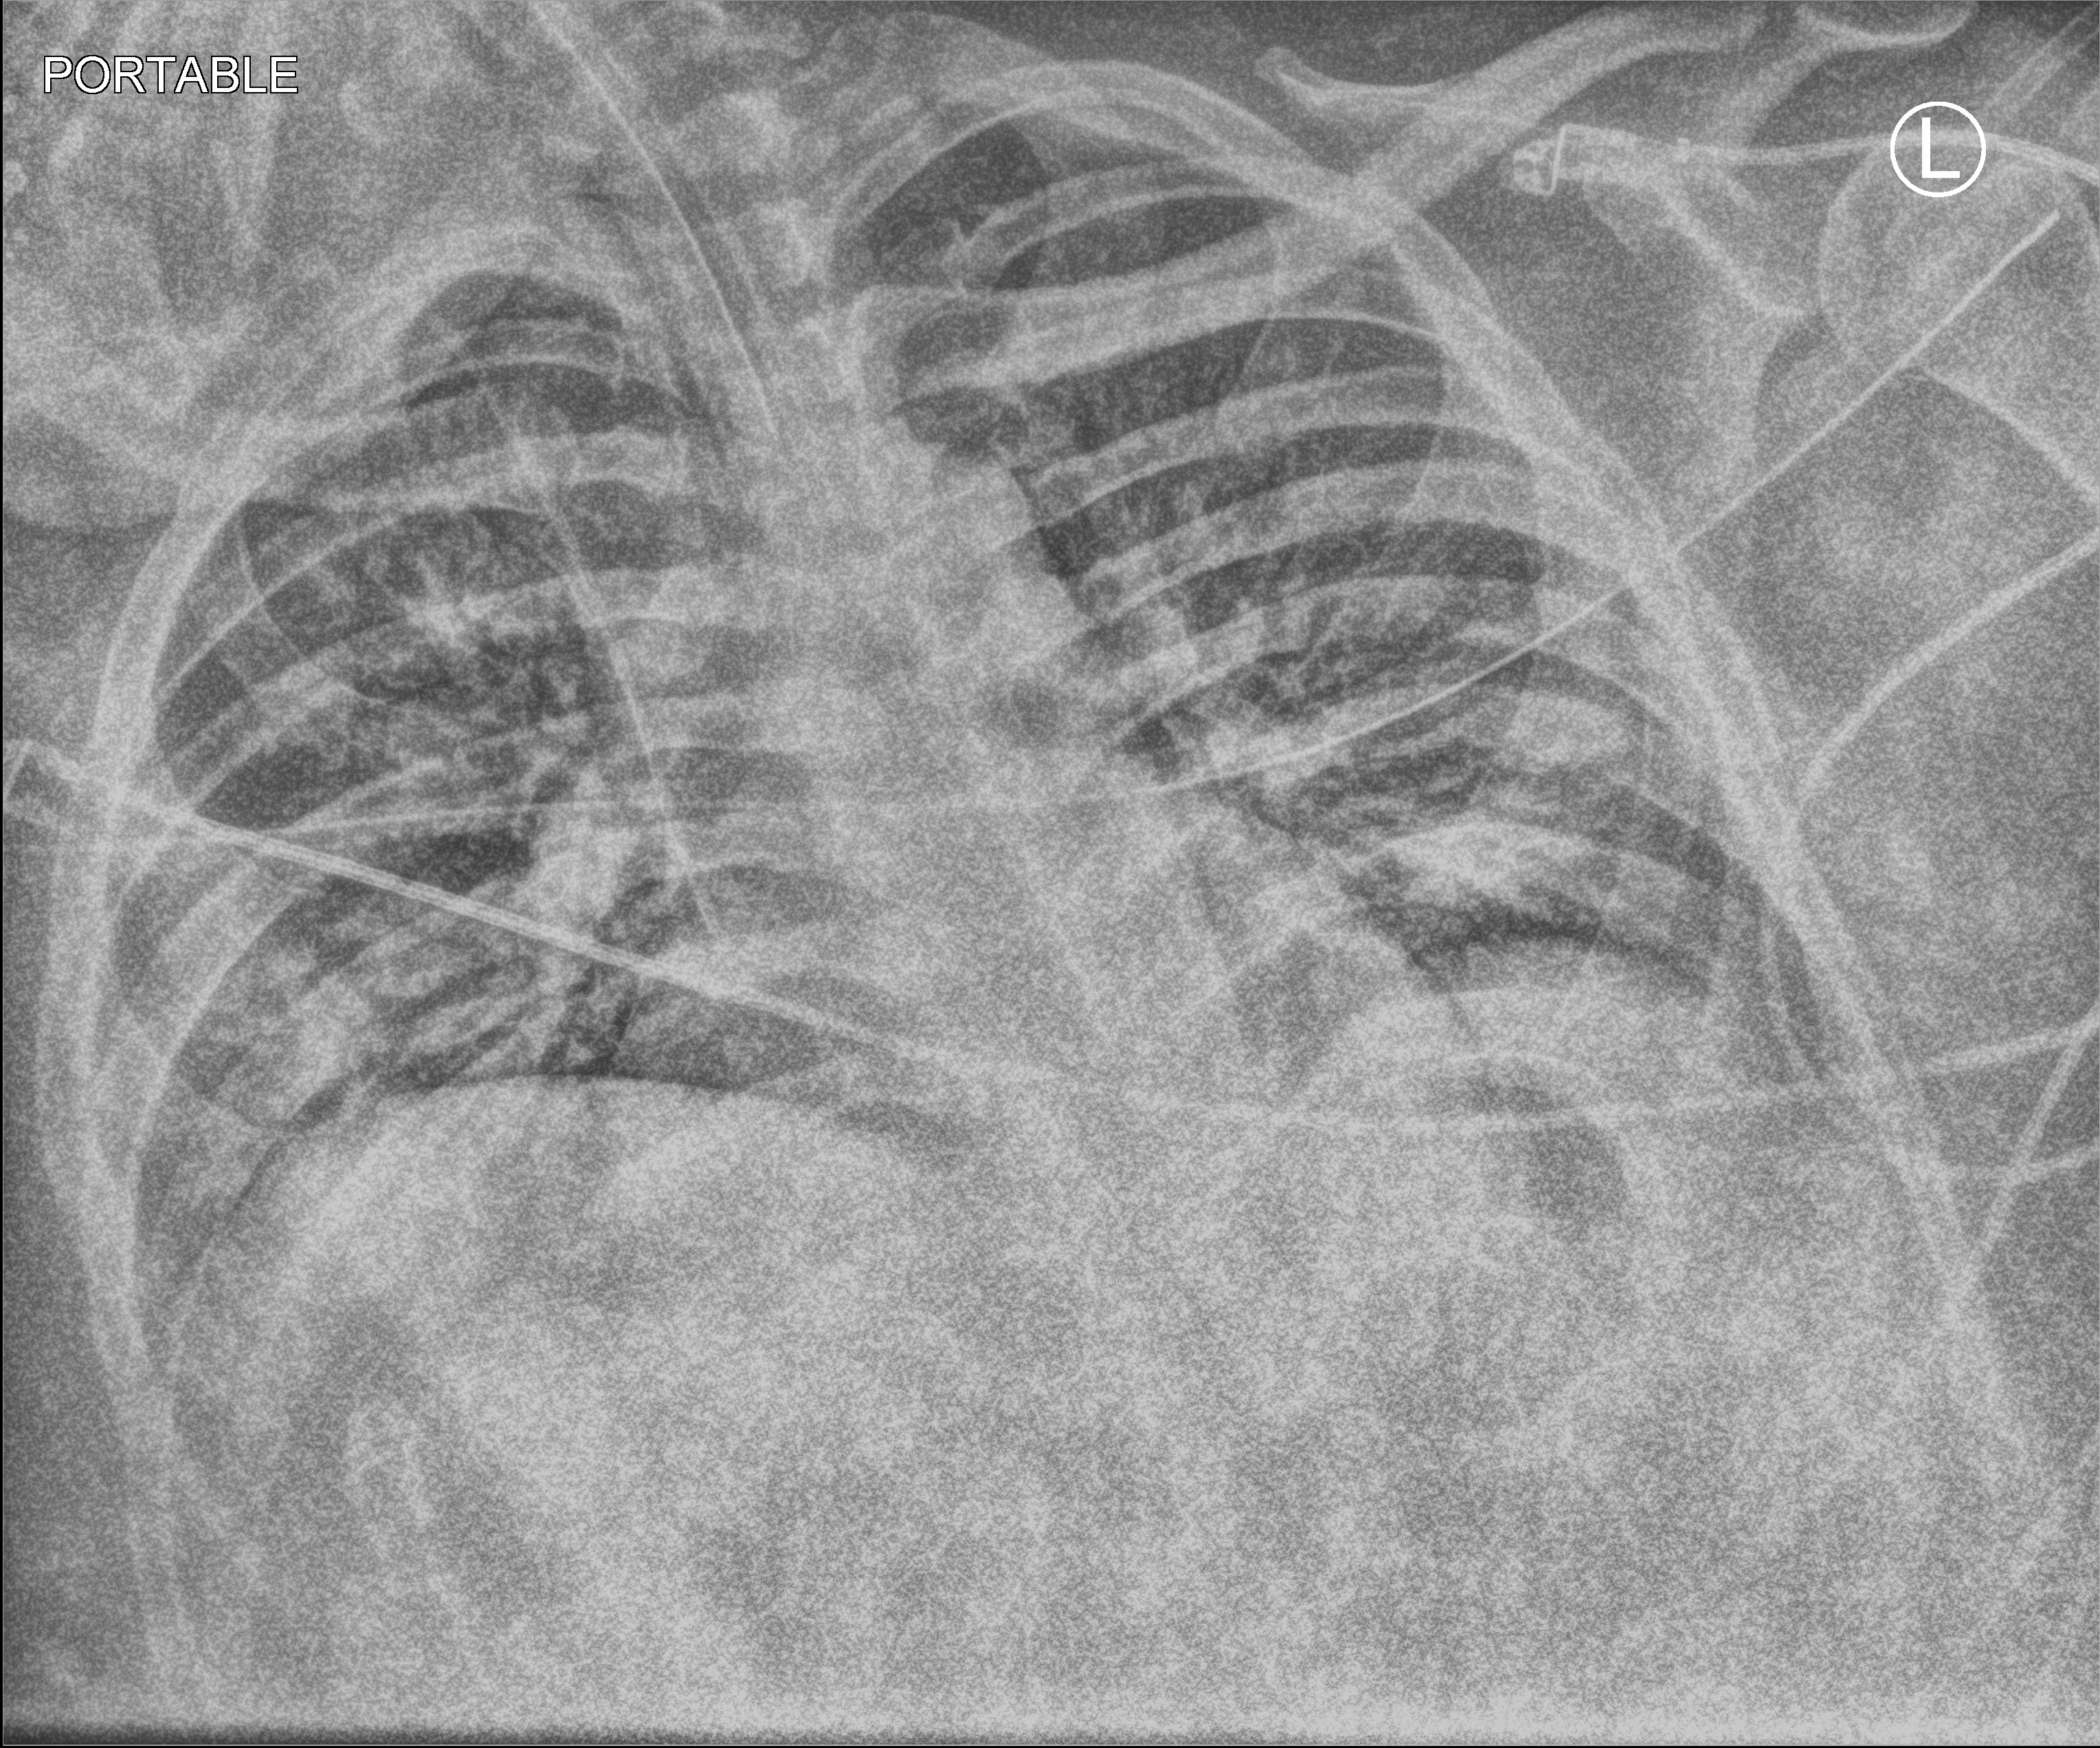
Chest X-ray (portable), anteroposterior (AP) projection. Patient hospitalised with COVID-19; male, aged 18–59 years.
From the hospital-stay record, not from the radiograph (when in the stay this image was taken is not recorded):
- mechanically ventilated during this hospital stay: yes